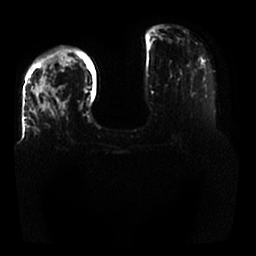
Breast MRI, one axial slice. Slice 8 of 25 in the series (ordered by position). Diffusion-weighted series; image 2 of 4 stored at this slice position (different b-values; order by instance number). 1.5 T. 4 mm slice thickness. 256 × 256 image matrix. Female patient.
Outlined on this slice (expert manual segmentation):
- tumour on diffusion-weighted imaging: box from (x=33, y=56) to (x=70, y=113) px